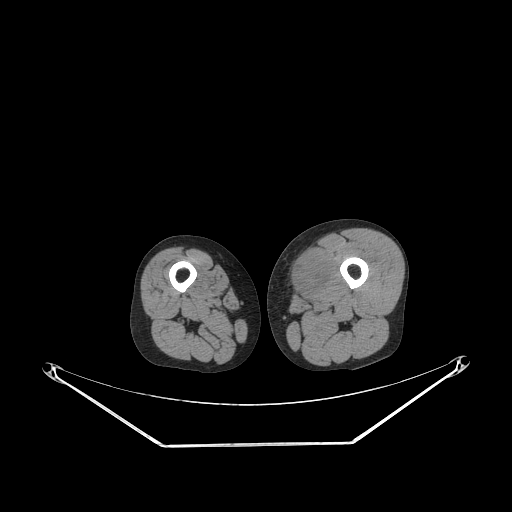
CT of an extremity soft-tissue mass (from a PET/CT study), one axial slice; slice 223 of 267 in the series (ordered by position); 140 kVp; soft-tissue window (W 400 / L 40 HU); 512 × 512 image matrix, field of view 500 × 500 mm. Male patient. Case-level facts recorded for this patient, not image findings: histological type: pleiomorphic leiomyosarcoma; grade: high; site of the primary tumour: left thigh.
Outlined on this slice (expert contour drawn on MRI and transferred to this co-registered scan by the dataset authors):
- gross tumour volume including surrounding oedema: bounding box [x1, y1, x2, y2] px = [286, 251, 330, 296]
- gross tumour volume (mass): [288, 253, 325, 295]